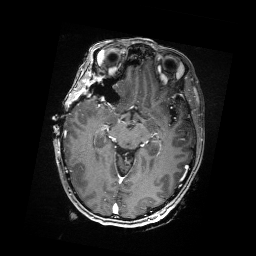
Brain MRI from a brain-tumour surgery series, one axial slice. Position 103 of 176 along the scan axis. T1-weighted post-contrast. 1 mm slice thickness. 256 × 256 image matrix. From the clinical record (not read from this slice): histopathology: Metastatic Carcinoma from Breast primary; tumour location: Right Frontal.
Annotated regions visible in this slice (expert manual segmentation):
- residual tumour: bounding box <99,92,105,96> (left, top, right, bottom; pixels)